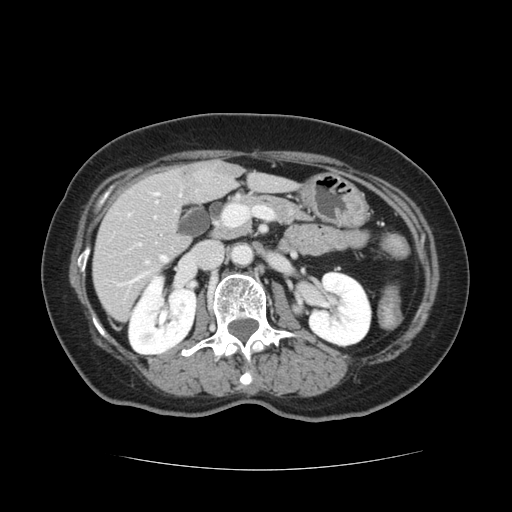
Contrast-enhanced abdominal CT, one axial slice. Position 52 of 128 along the scan axis. 120 kVp. Soft-tissue window (W 400 / L 40 HU). 2.5 mm slice thickness. 512 × 512 image matrix, field of view 366 × 366 mm. Female patient, age 67 years. From the clinical record (not read from this slice): diagnosis: colorectal cancer liver metastases, imaged before liver resection; multiple liver metastases: yes; largest metastasis: 3 cm; disease in both lobes: yes.
Annotated regions visible in this slice (expert manual segmentation):
- hepatic veins: bounding box [x1, y1, x2, y2] px = [116, 255, 167, 288]
- liver: [94, 162, 291, 320]
- planned liver remnant (the part of the liver to remain after resection): [95, 173, 291, 319]
- portal vein (with intrahepatic branches): [113, 207, 242, 264]